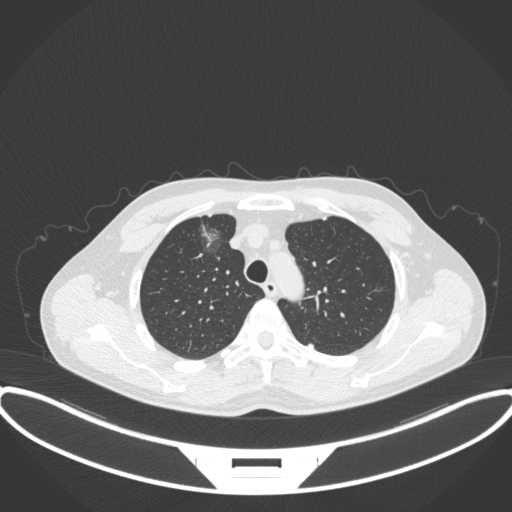
Chest CT, one axial slice. Position 286 of 395 along the scan axis. Reconstruction kernel B31f. 120 kVp. Lung window (W 1500 / L -600 HU). 1 mm slice thickness. 512 × 512 image matrix, field of view 424 × 424 mm. Patient: male, 60 years. From the clinical record (not read from this slice): clinical TNM (as recorded): T1c N0 M0.
Outlined on this slice (bounding box drawn by a radiologist):
- lung tumour (recorded histology: adenocarcinoma): bounding box <197,216,224,263> (left, top, right, bottom; pixels)